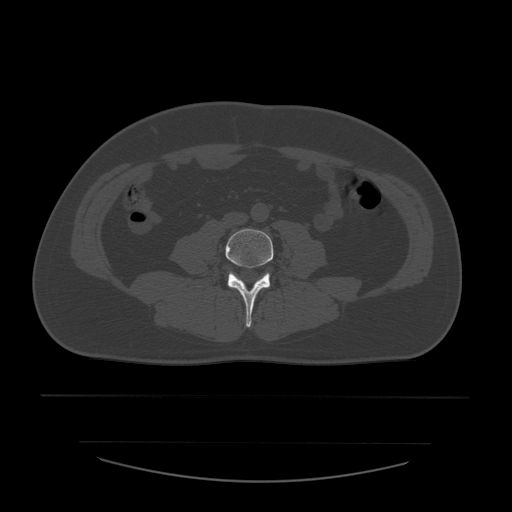
CT including the spine, one axial slice; slice 144 of 532 in the series (ordered by position); 120 kVp; bone window (W 1800 / L 400 HU); 1.25 mm slice thickness; 512 × 512 image matrix, field of view 441 × 441 mm. Patient age 44 years. Case-level facts recorded for this patient, not image findings: primary cancer: soft tissue sarcoma.
Annotated regions visible in this slice (semi-automatically segmented with operator editing):
- L4 vertebra: bounding box (x1, y1, x2, y2) in pixels: (226, 229, 274, 328)